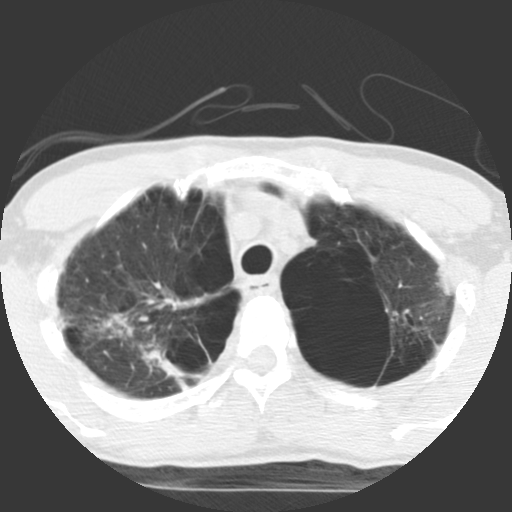
Axial slice from a low-dose chest CT screening exam, baseline annual screen, lung window (W 1500 / L -600 HU), 2.5 mm slice thickness, standard (soft-tissue) reconstruction kernel (STANDARD), slice 90 of 117 in the series, 512 × 512 image matrix, field of view 270 × 270 mm. Male participant, aged 62 years at enrolment.
Lesion marked by an expert reader, bounding box <117,319,213,391> (left, top, right, bottom; pixels). Screening reader's record for this exam: no non-calcified nodule ≥4 mm recorded. Participant outcome: lung cancer diagnosed 357 days after this screen — non-small cell carcinoma, right upper lobe, poorly differentiated (G3), stage IA (AJCC 6th edition), 70 mm at pathology.